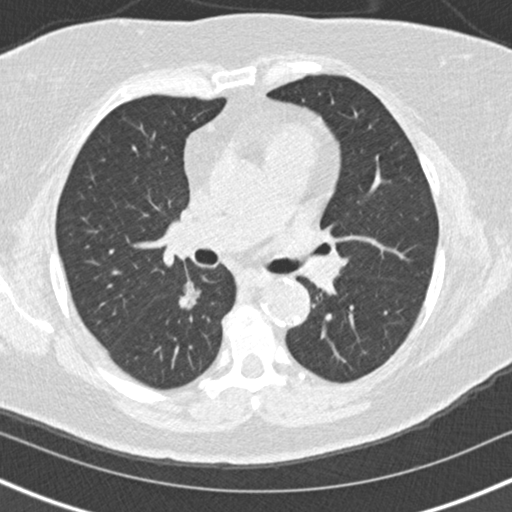
Low-dose screening chest CT, one axial slice. Position 92 of 152 along the scan axis. 120 kVp. Lung window (W 1500 / L -600 HU). 2 mm slice thickness. 512 × 512 image matrix, field of view 320 × 320 mm.
Structures marked on this image (expert manual segmentation):
- lesion 1 (tumor, lower lobe of right lung): box from (x=179, y=281) to (x=201, y=310) px